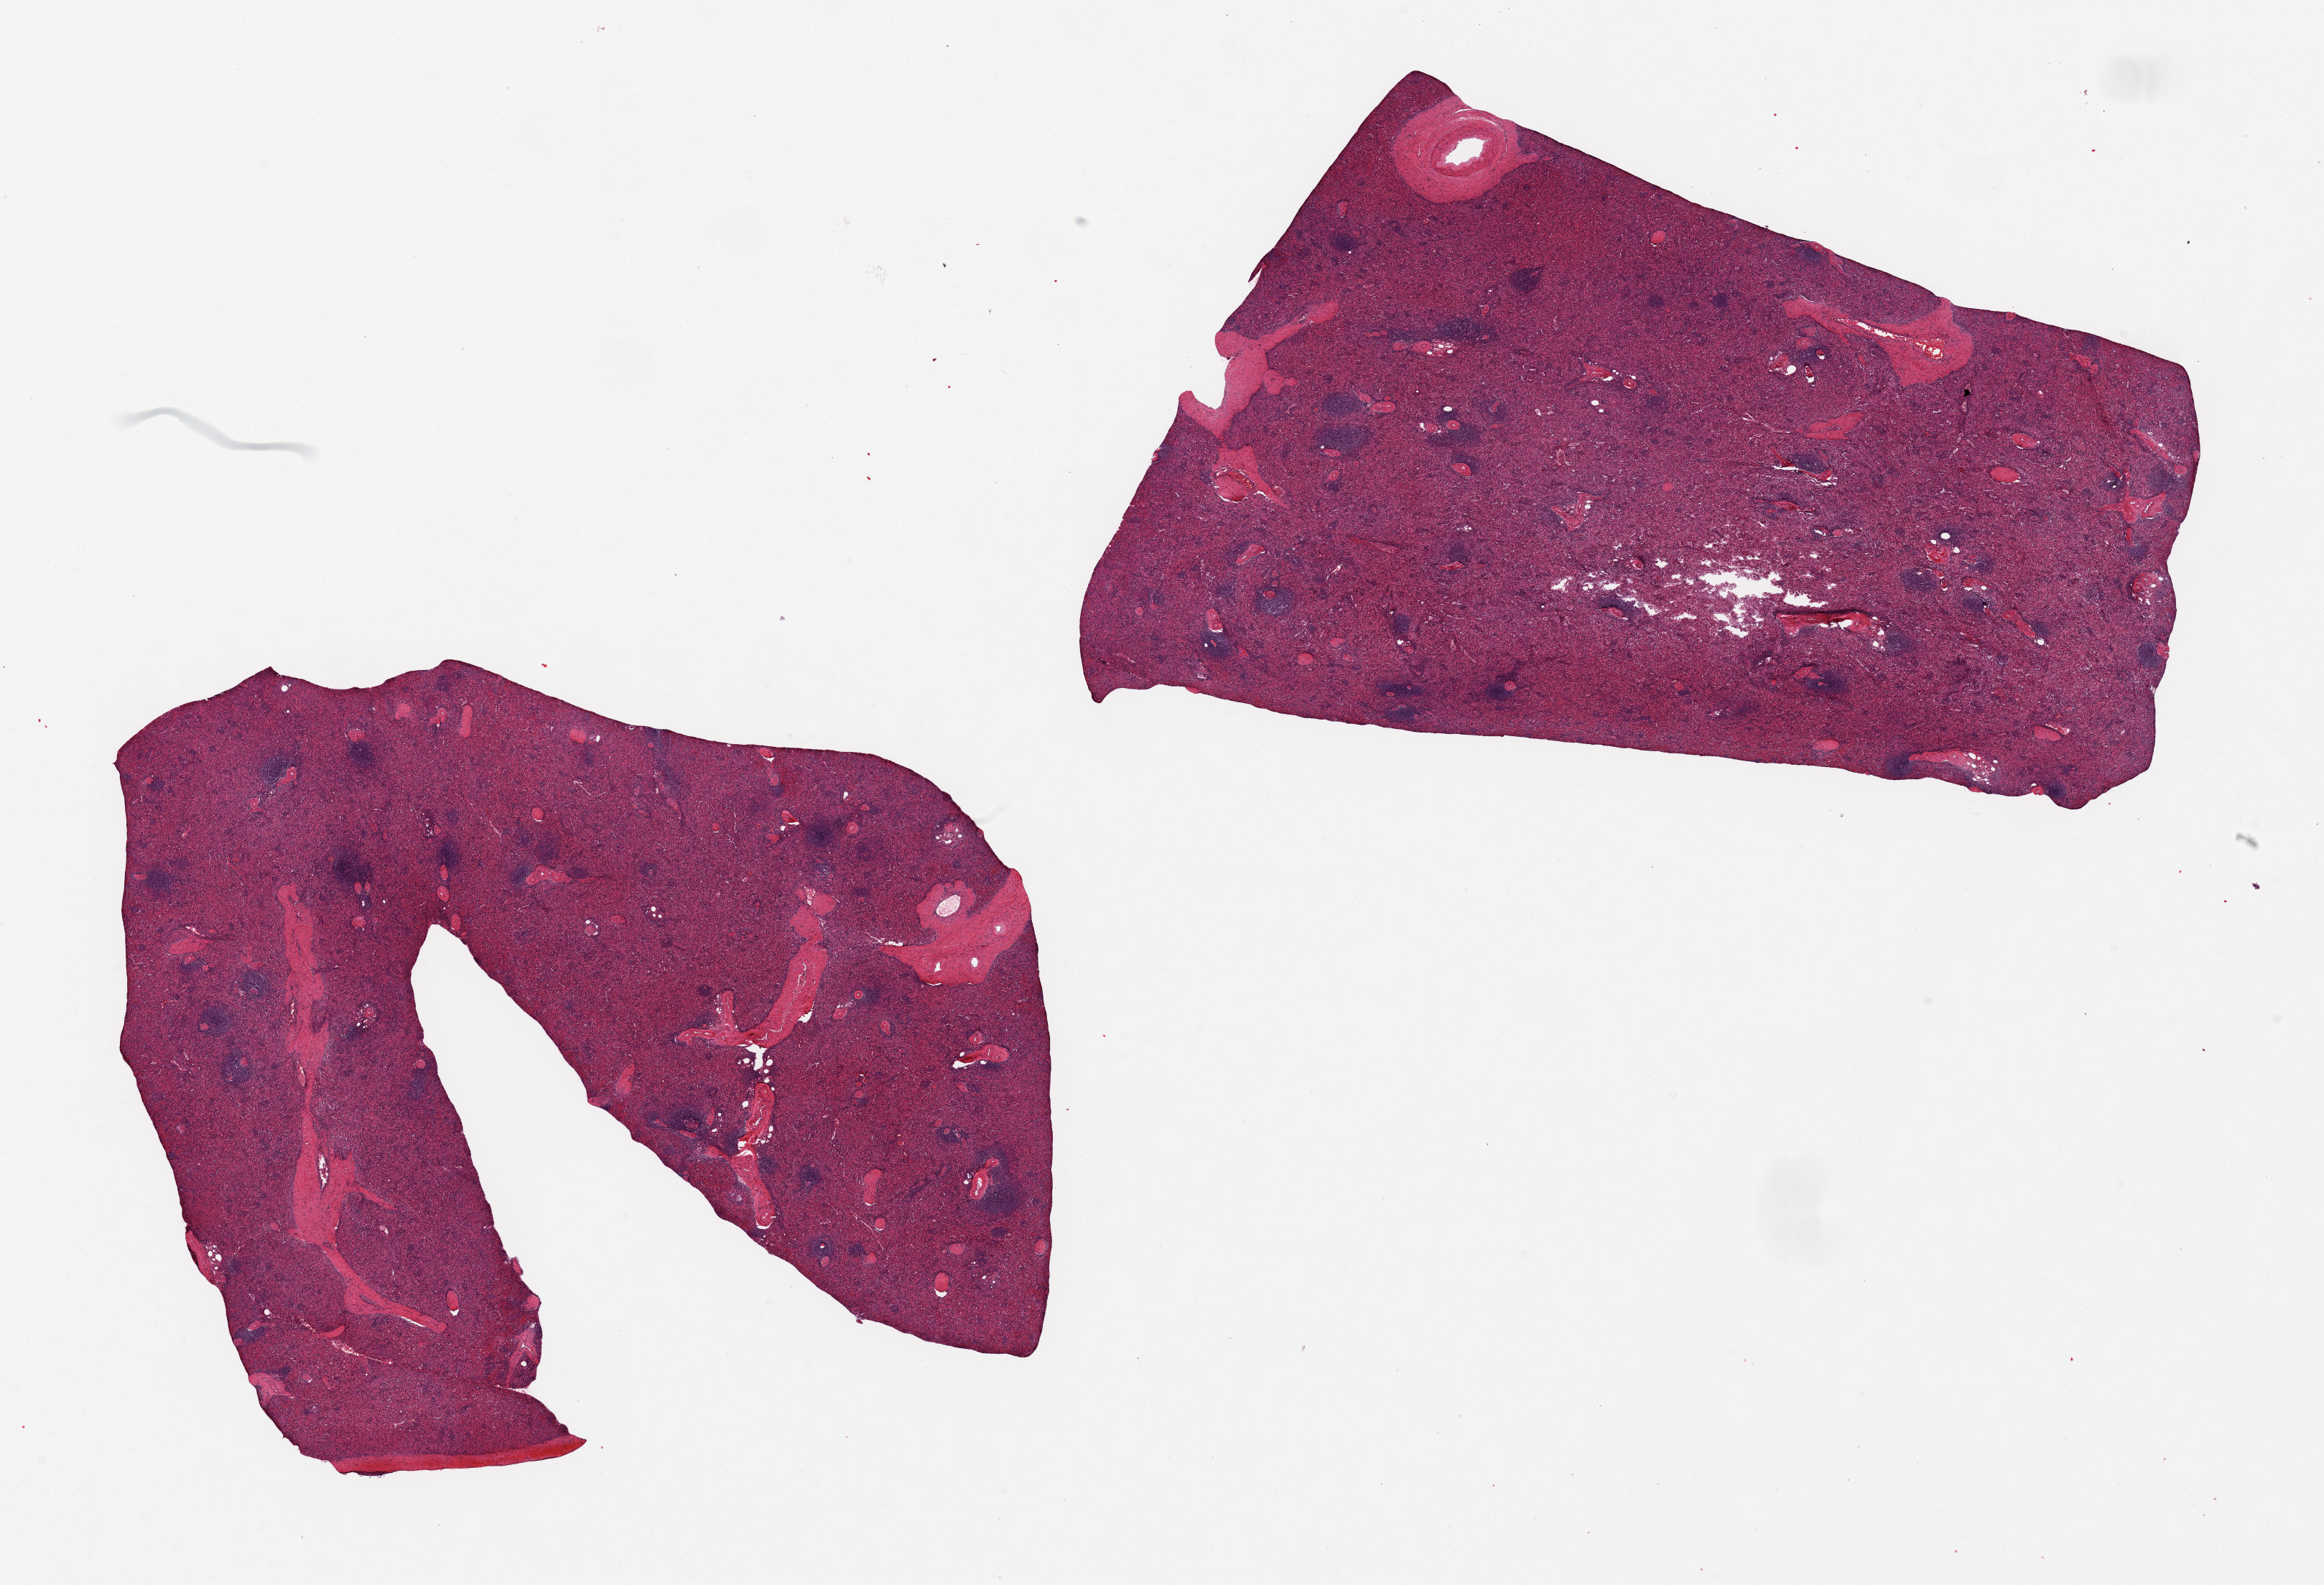
Whole-slide image, haematoxylin and eosin stain, a low-resolution overview of the entire scanned area, about 25.6 x 17.5 mm; PAXgene-fixed, paraffin-embedded tissue; section of spleen (target tissue); donor tissue sample. Male donor.
Review note (as recorded): 2 aliquots, ~10x6mm. Better preserved than usual, mild red pulp congestion.